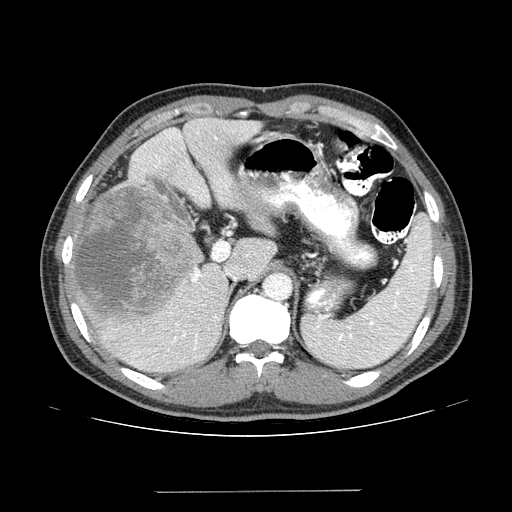
Contrast-enhanced abdominal CT (liver protocol), one axial slice; slice 93 of 131 in the series (ordered by position); reconstruction kernel STANDARD; 100 kVp; one of 2 acquisitions stored at this slice position; soft-tissue window (W 400 / L 40 HU); 2.5 mm slice thickness; 512 × 512 image matrix. Case-level facts recorded for this patient, not image findings: diagnosis: hepatocellular carcinoma (patient treated with transarterial chemoembolisation; whether this scan precedes or follows treatment is not stated here); TNM stage (as recorded): Stage-I; Child-Pugh class: A; tumour differentiation: poorly differentiated; tumour nodularity: uninodular.
Annotated regions visible in this slice (semi-automatic segmentation, software-assisted and operator-edited):
- liver parenchyma outside the tumour (the mass and vessels are separate outlines, so this box may not span the whole liver): bounding box (x1, y1, x2, y2) in pixels: (66, 118, 262, 372)
- mass: (70, 183, 200, 322)
- liver vessels: (132, 128, 256, 366)